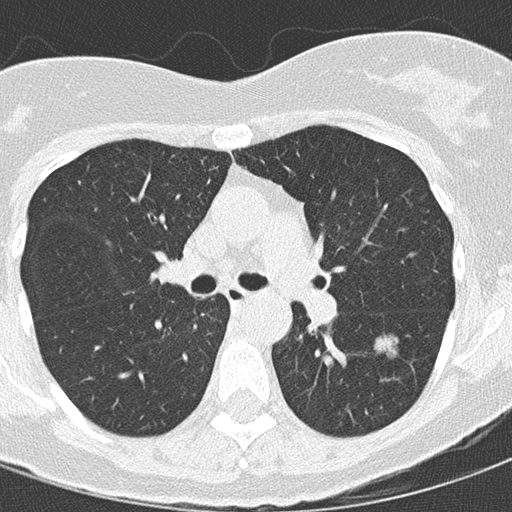
Chest CT (low-dose screening protocol), one axial image; first (baseline) screen; lung window (W 1500 / L -600 HU); 2 mm slice thickness. Female participant, aged 68 years at enrolment.
Expert-annotated lung lesion, bounding box [x1, y1, x2, y2] px = [368, 322, 414, 366]. Screening reader's record for this exam (one nodule recorded; not confirmed to be the boxed lesion): non-calcified nodule or mass ≥4 mm, left lower lobe, 15 × 15 mm, mixed attenuation. Official screen result: positive, change unspecified: nodule(s) >= 4 mm or enlarging nodule(s), mass(es), or other non-specific abnormalities suspicious for lung cancer. Lung cancer was diagnosed 72 days after this screen: bronchiolo-alveolar adenocarcinoma, NOS, left lower lobe, stage IIIB (AJCC 6th edition), 12 mm at pathology.